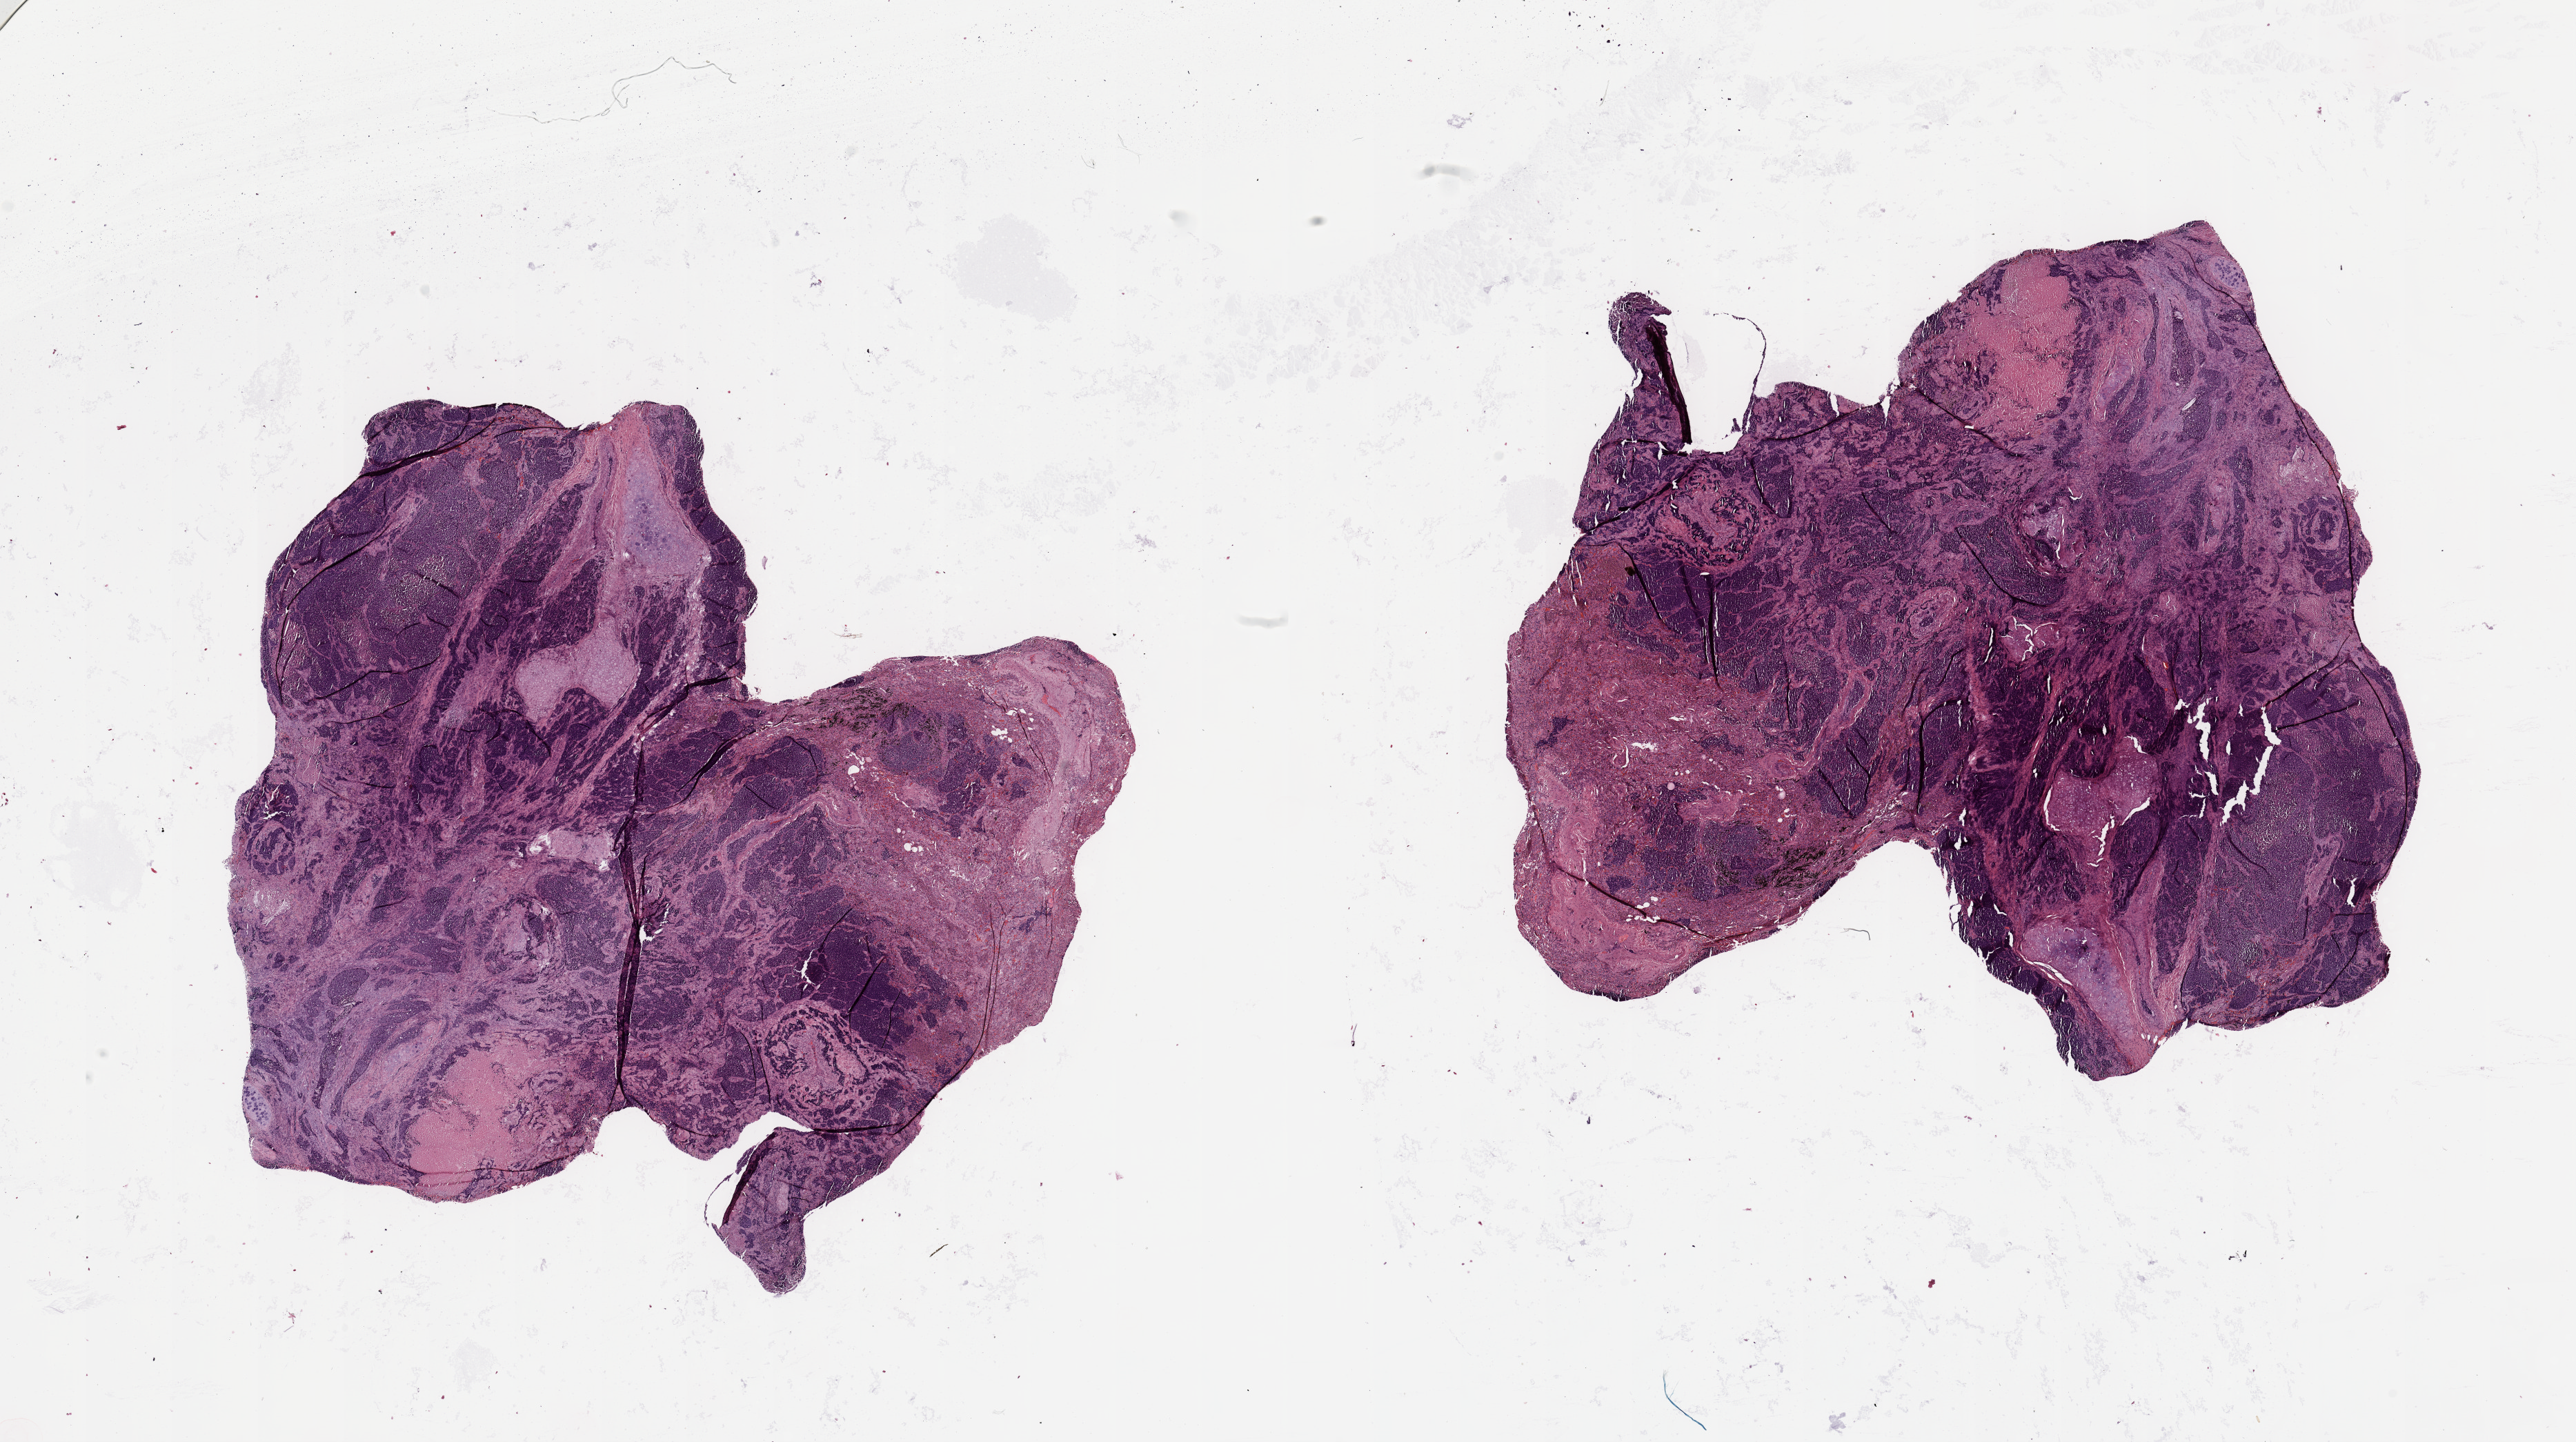
Digitized H&E tissue section (whole slide), shown as a low-resolution overview of the whole scanned area (about 29.5 x 16.5 mm, from a 20x scan), tumour tissue sample, lung. Male, 63 y/o.
Primary tumour site (as recorded): left upper lobe. Patient diagnosis (cohort enrolment): squamous cell carcinoma (lung).